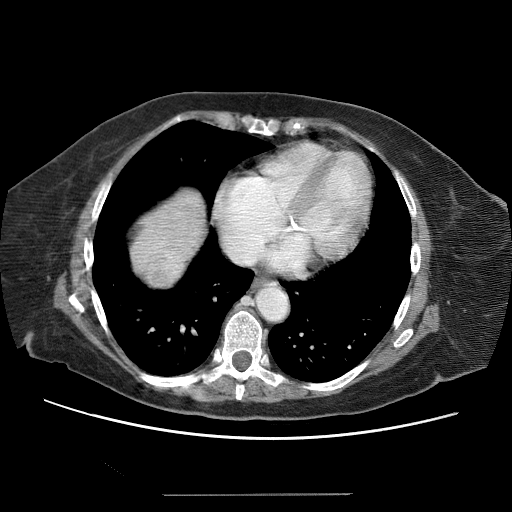
Contrast-enhanced abdominal CT (liver protocol), one axial slice. Position 61 of 65 along the scan axis. Soft-tissue window (W 400 / L 40 HU). 512 × 512 image matrix, field of view 380 × 380 mm. Case-level facts recorded for this patient, not image findings: diagnosis: hepatocellular carcinoma (patient treated with transarterial chemoembolisation; whether this scan precedes or follows treatment is not stated here); TNM stage (as recorded): Stage-IIIB; Child-Pugh class: A.
Outlined on this slice (semi-automatic segmentation, software-assisted and operator-edited):
- abdominal aorta: bounding box [x1, y1, x2, y2] px = [259, 289, 289, 322]
- liver parenchyma outside the tumour (the mass and vessels are separate outlines, so this box may not span the whole liver): [138, 192, 200, 276]
- mass: [139, 239, 173, 279]
- liver vessels: [166, 262, 175, 273]